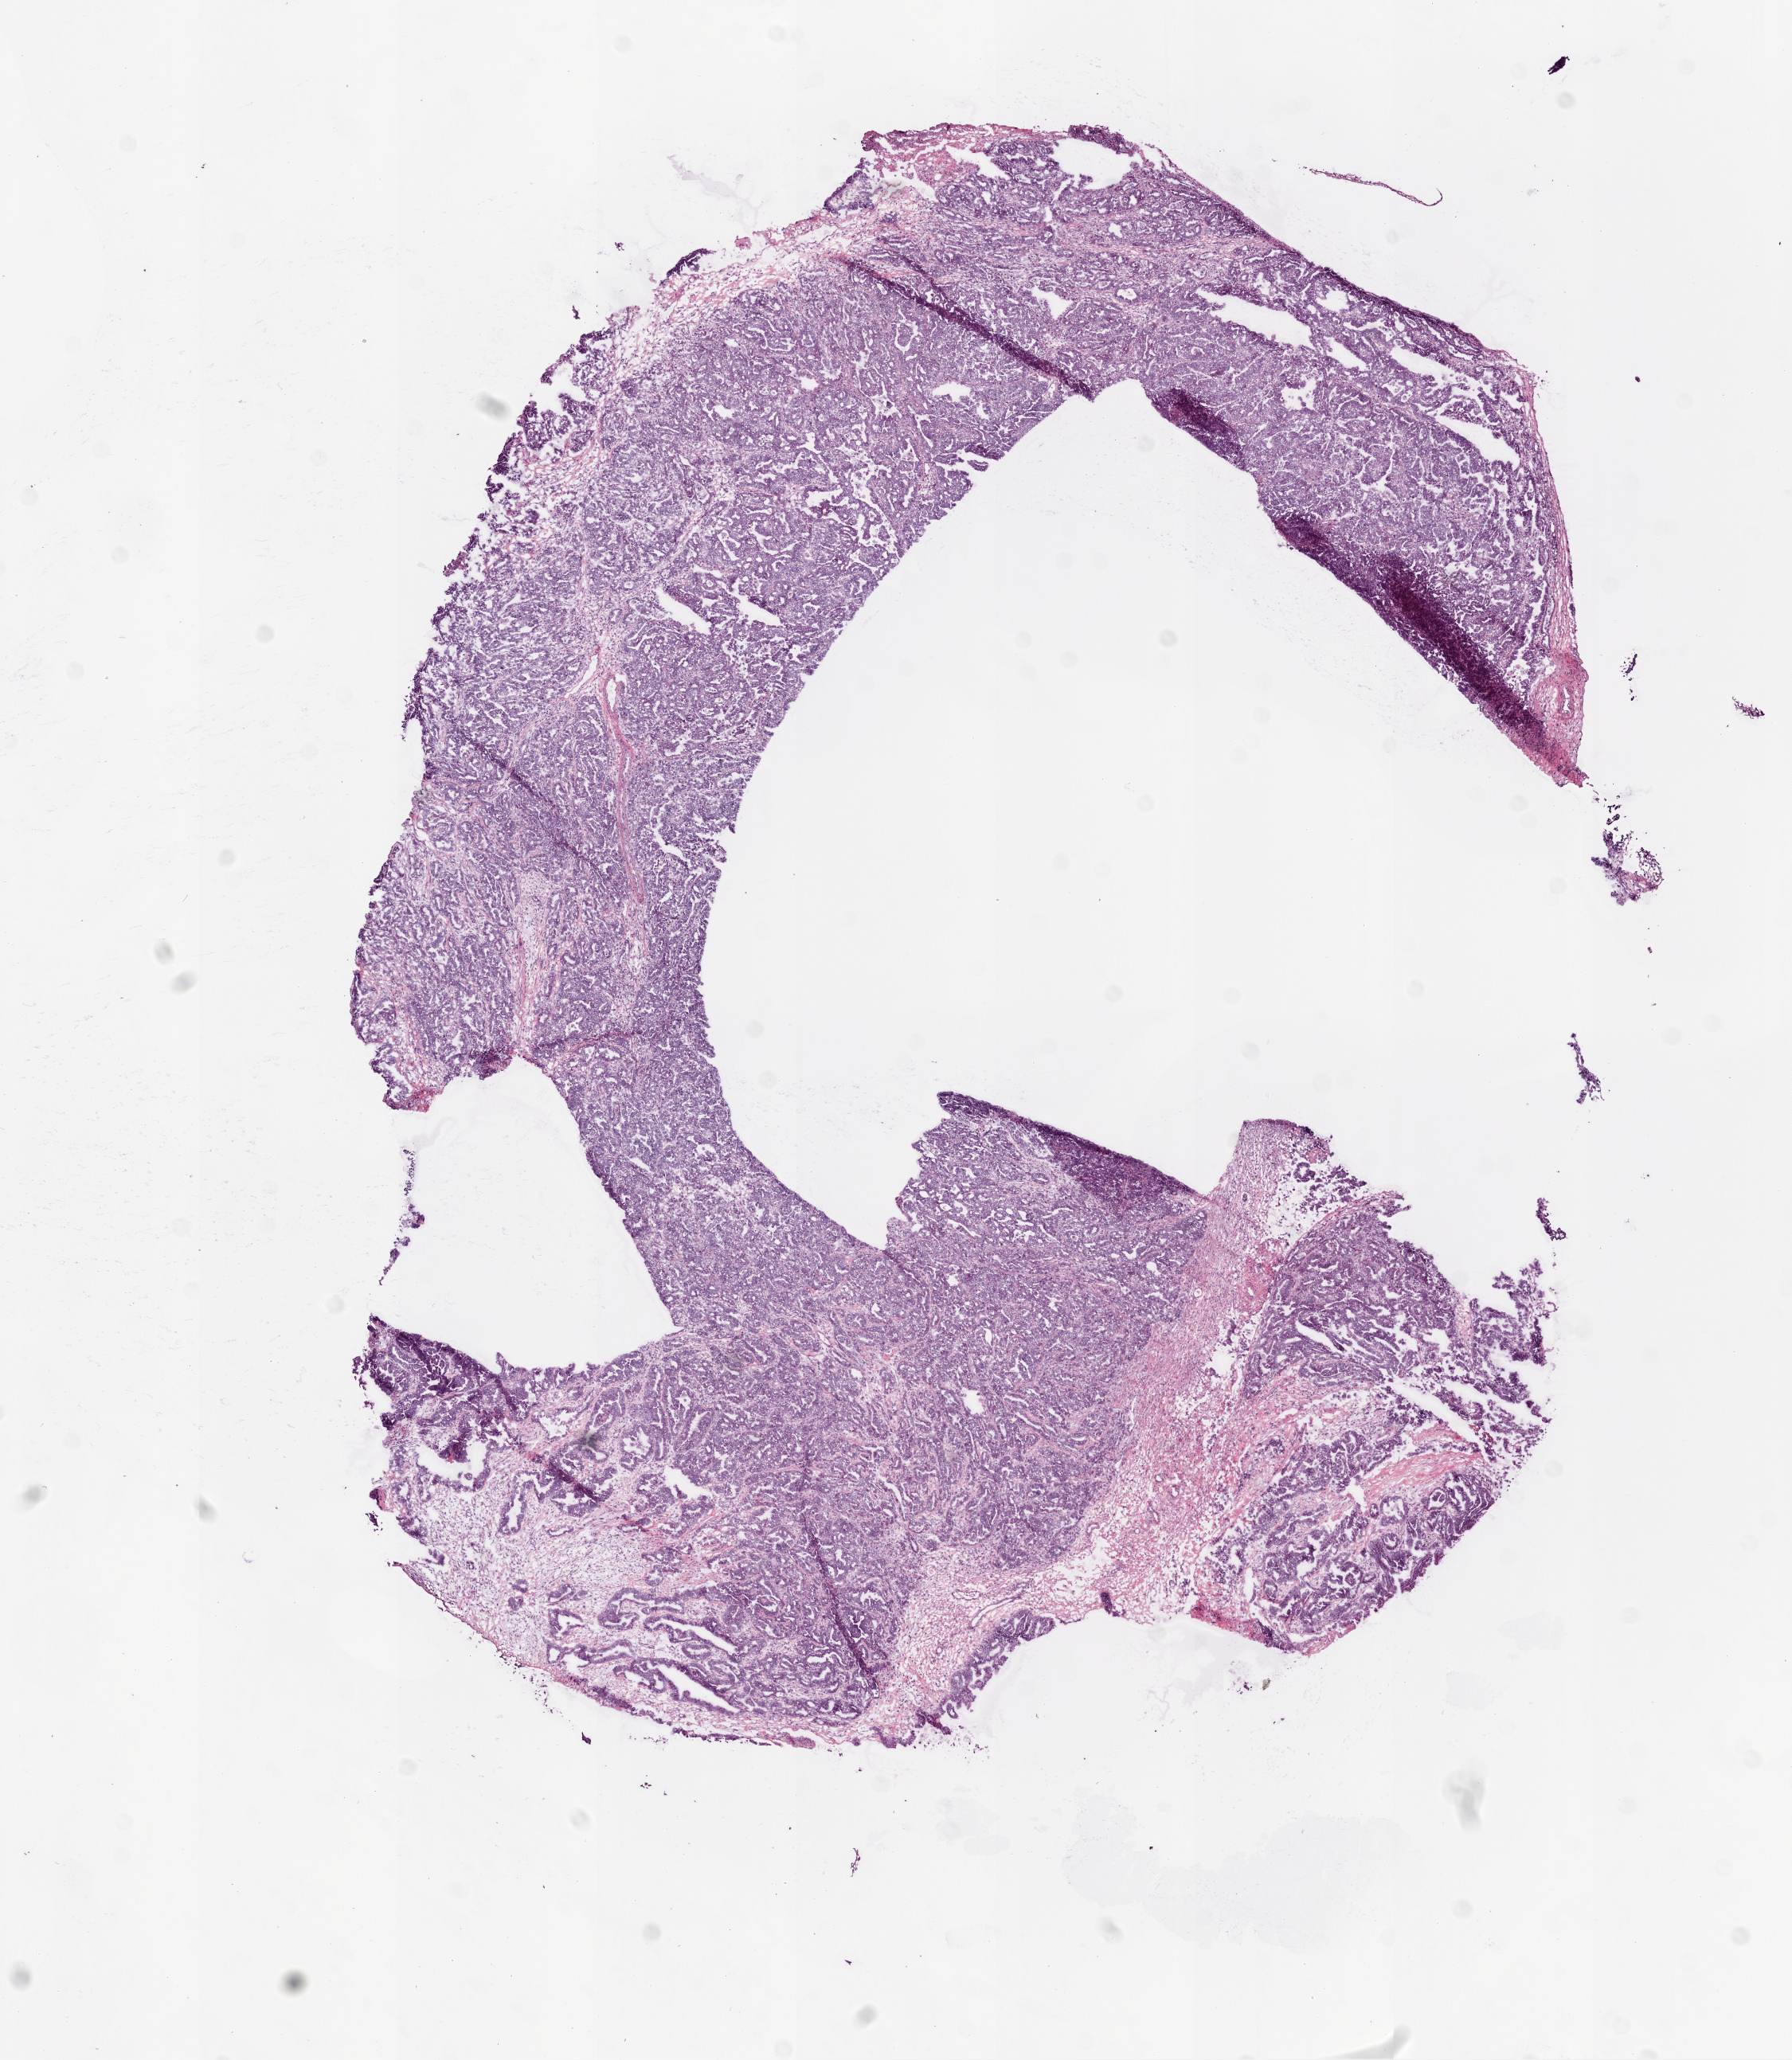
Digitized H&E-stained tissue section (whole slide), low-resolution overview of the scanned area, about 9.0 x 10.4 mm. Frozen section from the bottom of the tissue portion. Ovary, primary tumour sample. Female patient; age at initial diagnosis 42 years. Histologic grade: G3 (poorly differentiated). Slide review estimates, as recorded: tumour cells 95%, tumour nuclei 99%, normal cells 0%, stromal cells 5%, necrosis 0%.
Diagnosis: Serous cystadenocarcinoma, NOS. Laterality: bilateral. FIGO stage: IIIC.